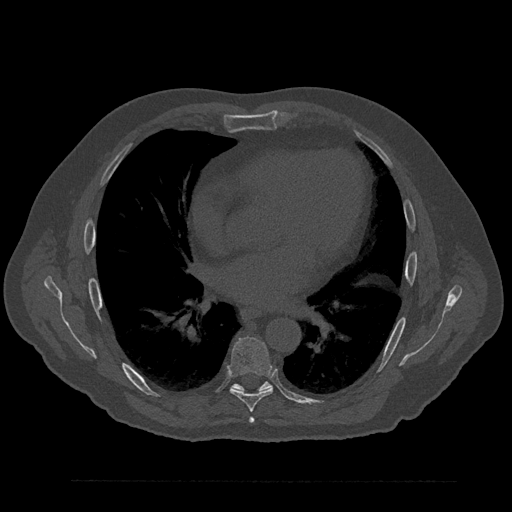
CT including the spine, one axial slice. Slice 492 of 797 in the series (ordered by position). 120 kVp. Bone window (W 1800 / L 400 HU). 0.5 mm slice thickness. 512 × 512 image matrix. Male patient, age 61 years. From the clinical record (not read from this slice): primary cancer: prostate.
Annotated regions visible in this slice (semi-automatic segmentation, software-assisted and operator-edited):
- T6 vertebra: bounding box [x1, y1, x2, y2] px = [249, 417, 255, 423]
- T7 vertebra: [228, 336, 273, 412]
- T8 vertebra: [232, 382, 272, 392]